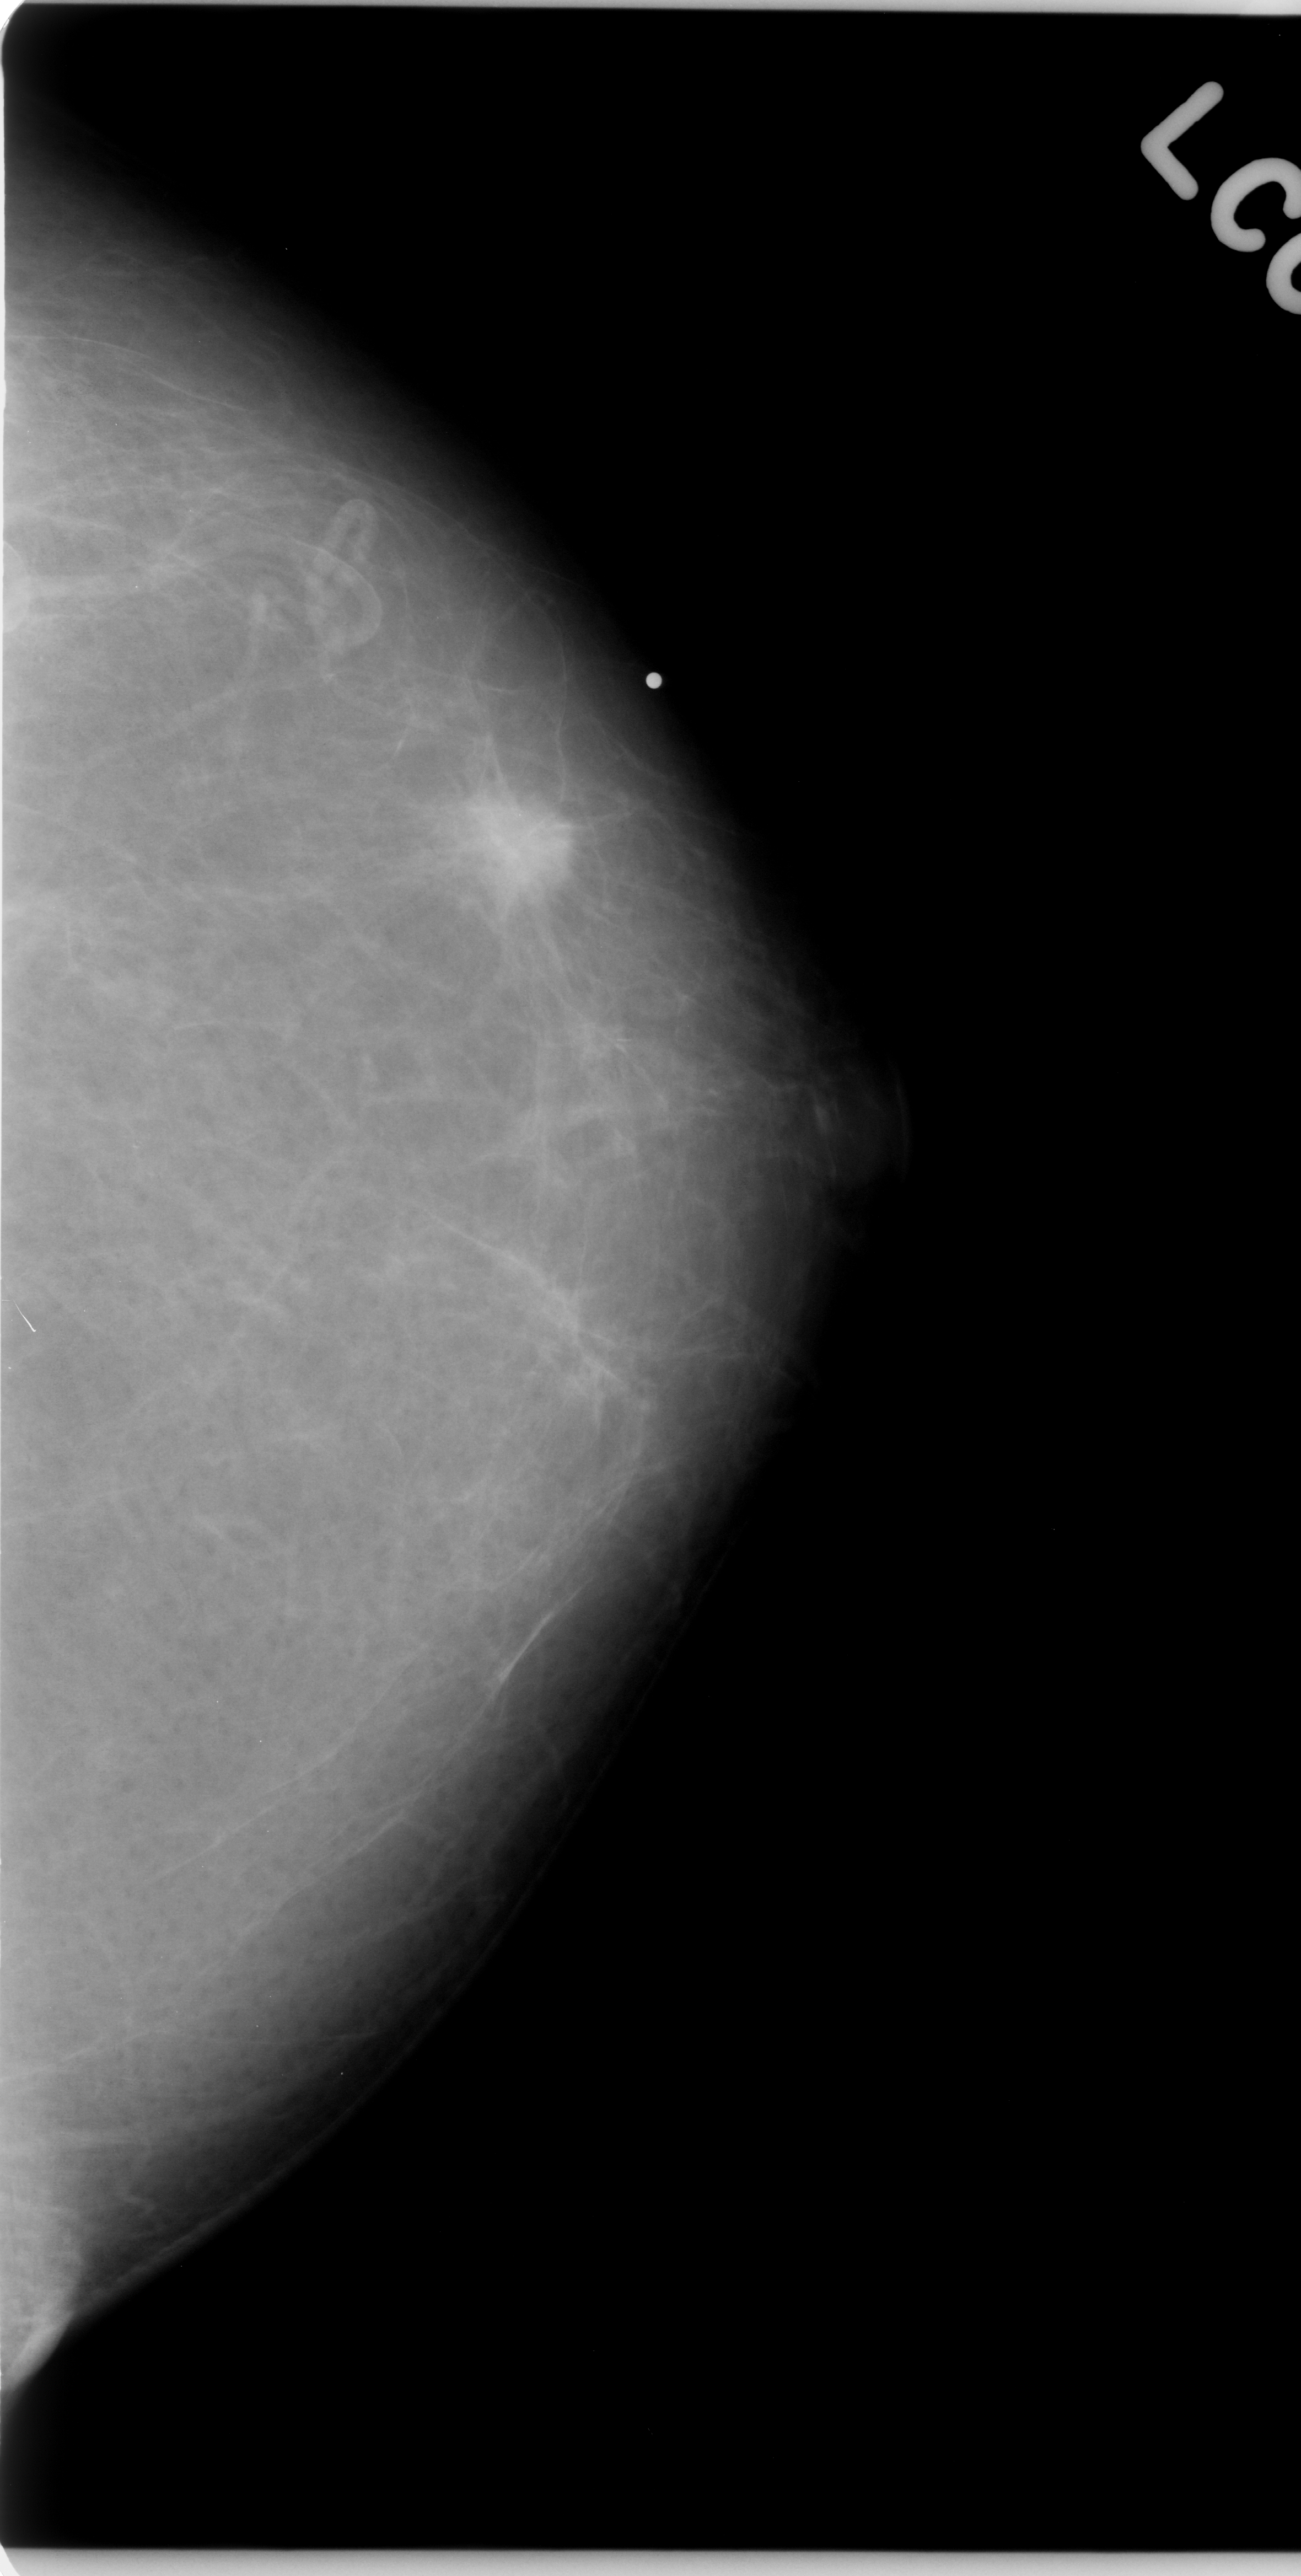
Scanned film-screen mammogram, left breast, craniocaudal (CC) view, BI-RADS breast density category 1 (scale 1–4).
- Abnormality record for this image: mass, shape irregular, margins spiculated; BI-RADS assessment category 5; subtlety rating 5 on a 1 (subtle) to 5 (obvious) scale; pathology (as recorded): malignant.